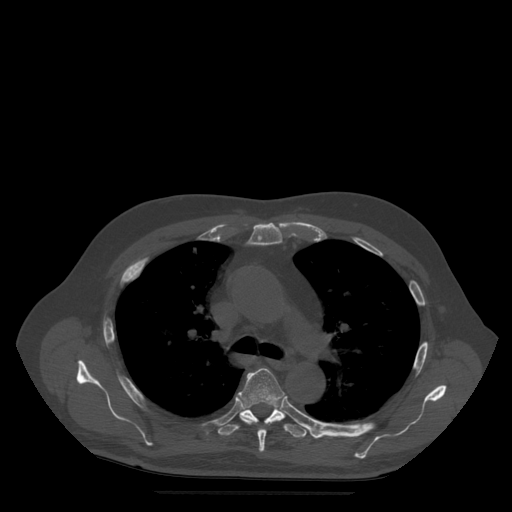
CT including the spine, one axial slice. Bone window (W 1800 / L 400 HU). 1.25 mm slice thickness. 512 × 512 image matrix. Patient age 72 years. From the clinical record (not read from this slice): primary cancer: prostate.
Annotated regions visible in this slice (semi-automatic segmentation, software-assisted and operator-edited):
- T5 vertebra: bounding box (x1, y1, x2, y2) in pixels: (238, 369, 286, 452)
- T6 vertebra: (218, 404, 307, 438)